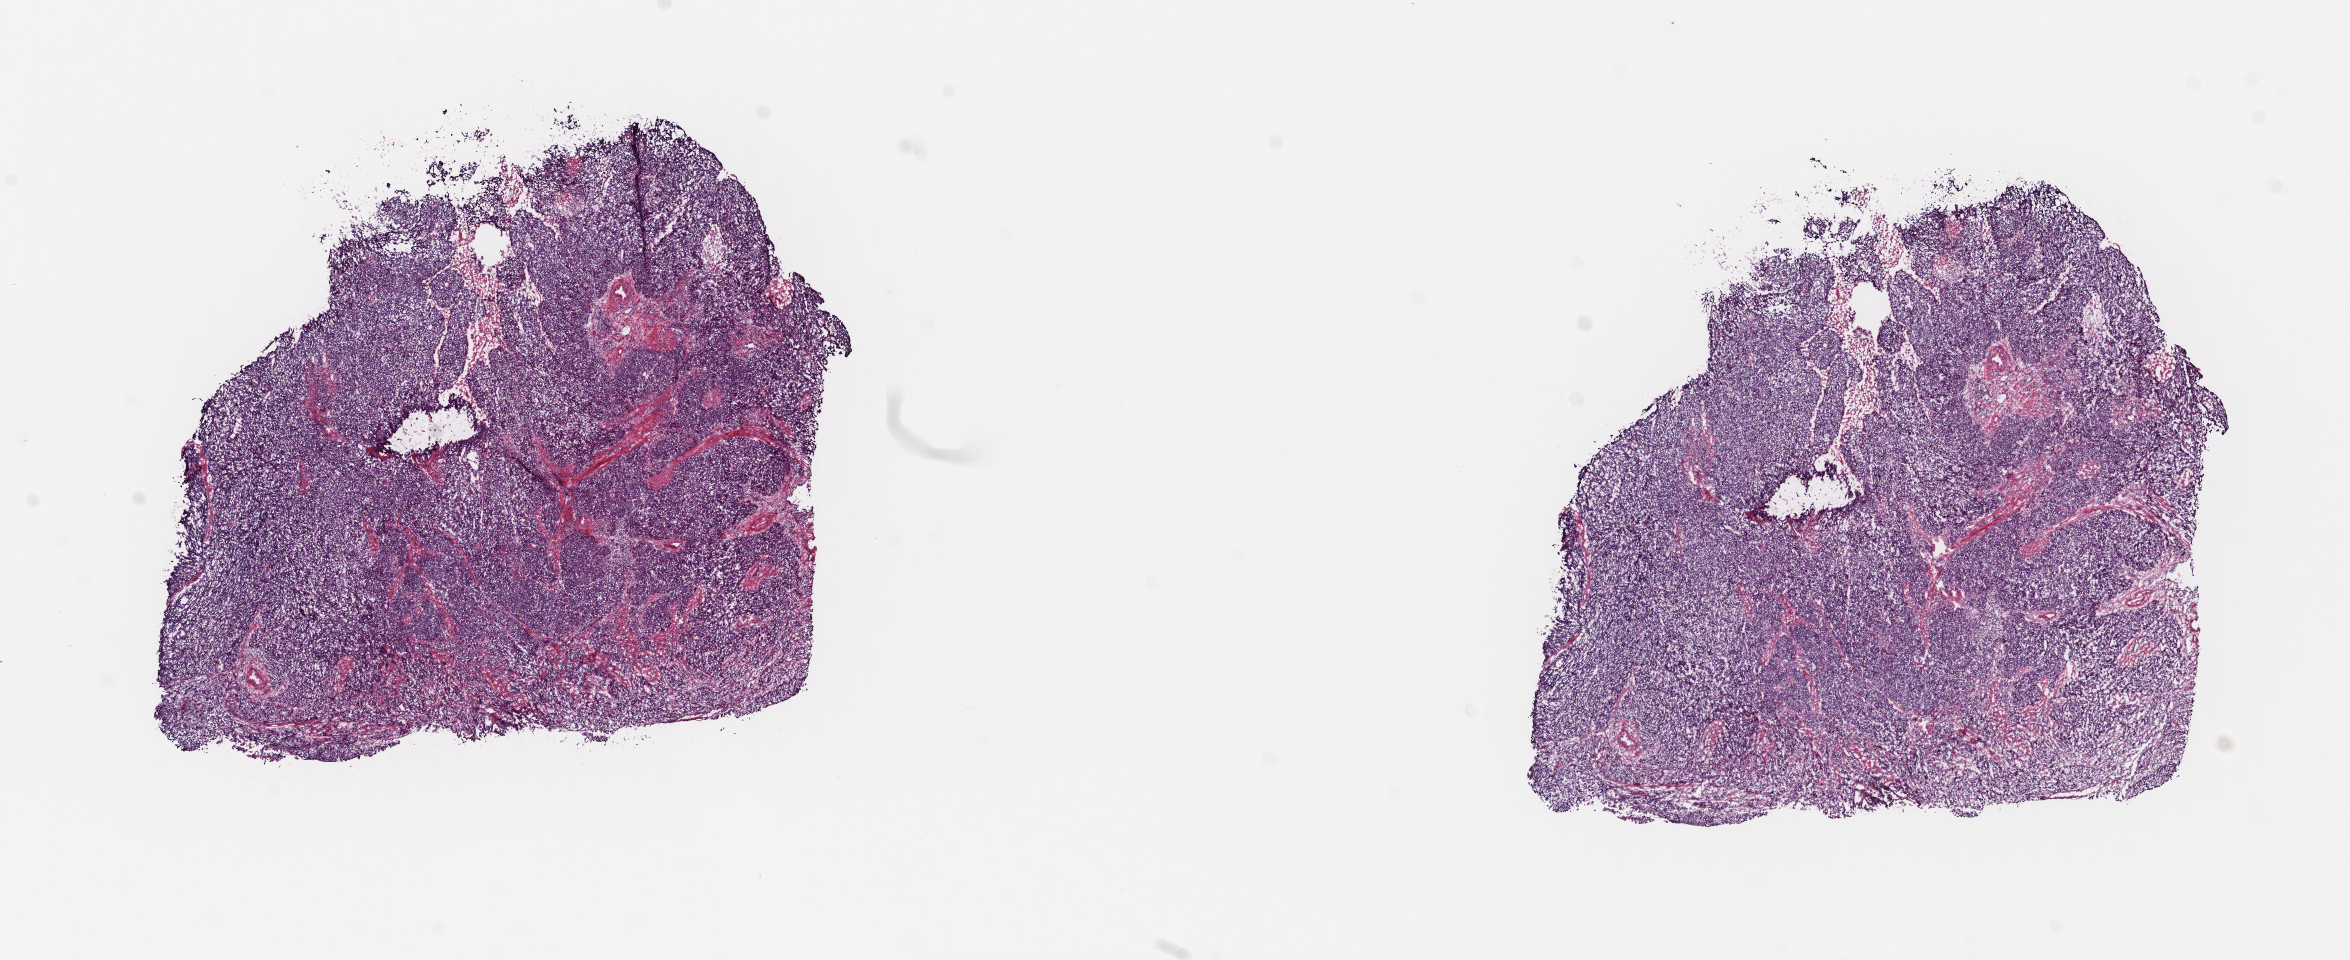
Whole-slide histology image, Hematoxylin and eosin (H&E) stained, a low-resolution overview of the entire scanned area, about 18.5 x 7.5 mm, frozen section, primary tumour sample from the cervix. Patient: female, age at initial diagnosis 54 years. Histologic grade: G2 (moderately differentiated). Composition of this section per pathologist review: tumour cells 100%, tumour nuclei 90%, normal cells 0%, stromal cells 0%, necrosis 0%. Inflammatory infiltration, as recorded: lymphocyte infiltration 0%, monocyte infiltration 0%, neutrophil infiltration 0%.
• diagnosis: Squamous cell carcinoma, NOS (cervix uteri)
• lymph nodes positive (case pathology): 3 of 39 examined
• FIGO stage: IB1